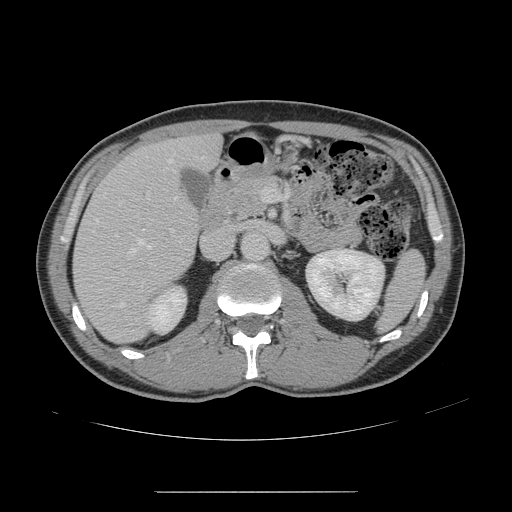
Contrast-enhanced abdominal CT, one axial slice. Position 76 of 178 along the scan axis. 120 kVp. Soft-tissue window (W 400 / L 40 HU). 2.5 mm slice thickness. 512 × 512 image matrix, field of view 401 × 401 mm. Male patient, age 53 years. Case-level facts recorded for this patient, not image findings: diagnosis: colorectal cancer liver metastases, imaged before liver resection; multiple liver metastases: yes; largest metastasis: 2.4 cm; chemotherapy before resection: yes.
Outlined on this slice (manually delineated by an expert):
- hepatic veins: box from (x=96, y=159) to (x=172, y=308) px
- liver: (x=73, y=136)–(x=221, y=343)
- planned liver remnant (the part of the liver to remain after resection): (x=172, y=136)–(x=220, y=165)
- portal vein (with intrahepatic branches): (x=147, y=187)–(x=267, y=202)